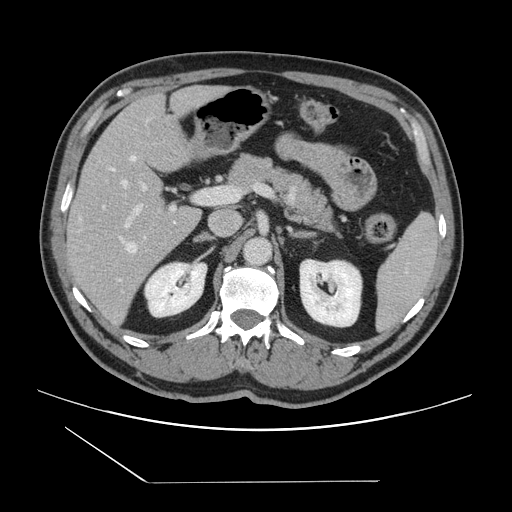
Contrast-enhanced abdominal CT, one axial slice; slice 80 of 157 in the series (ordered by position); intravenous contrast given; soft-tissue window (W 400 / L 40 HU); 2.5 mm slice thickness; 512 × 512 image matrix, field of view 407 × 407 mm. Male patient, age 61 years. Case-level facts recorded for this patient, not image findings: diagnosis: colorectal cancer liver metastases, imaged before liver resection; multiple liver metastases: yes.
Structures marked on this image (expert manual segmentation):
- hepatic veins: bounding box (x1, y1, x2, y2) in pixels: (110, 156, 137, 280)
- liver: (68, 86, 223, 330)
- planned liver remnant (the part of the liver to remain after resection): (69, 87, 221, 220)
- portal vein (with intrahepatic branches): (103, 183, 206, 227)